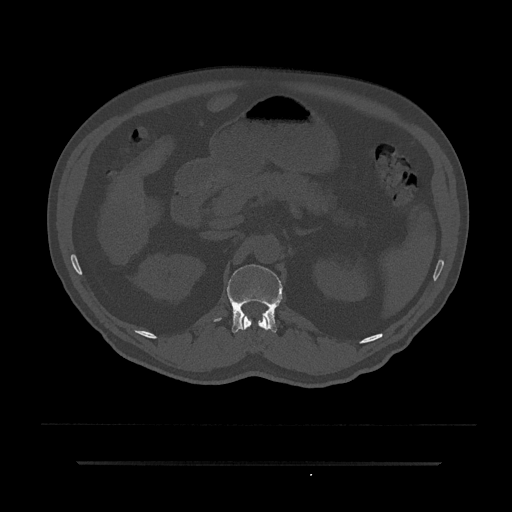
CT including the spine, one axial slice. Position 168 of 797 along the scan axis. Reconstruction kernel Br40s/3. 120 kVp. Bone window (W 1800 / L 400 HU). 512 × 512 image matrix, field of view 464 × 464 mm. Male patient, age 59 years. From the clinical record (not read from this slice): primary cancer: bile ducts.
Structures marked on this image (semi-automatic segmentation, software-assisted and operator-edited):
- L1 vertebra: bounding box <214,264,283,334> (left, top, right, bottom; pixels)
- T12 vertebra: <241,315,268,347>